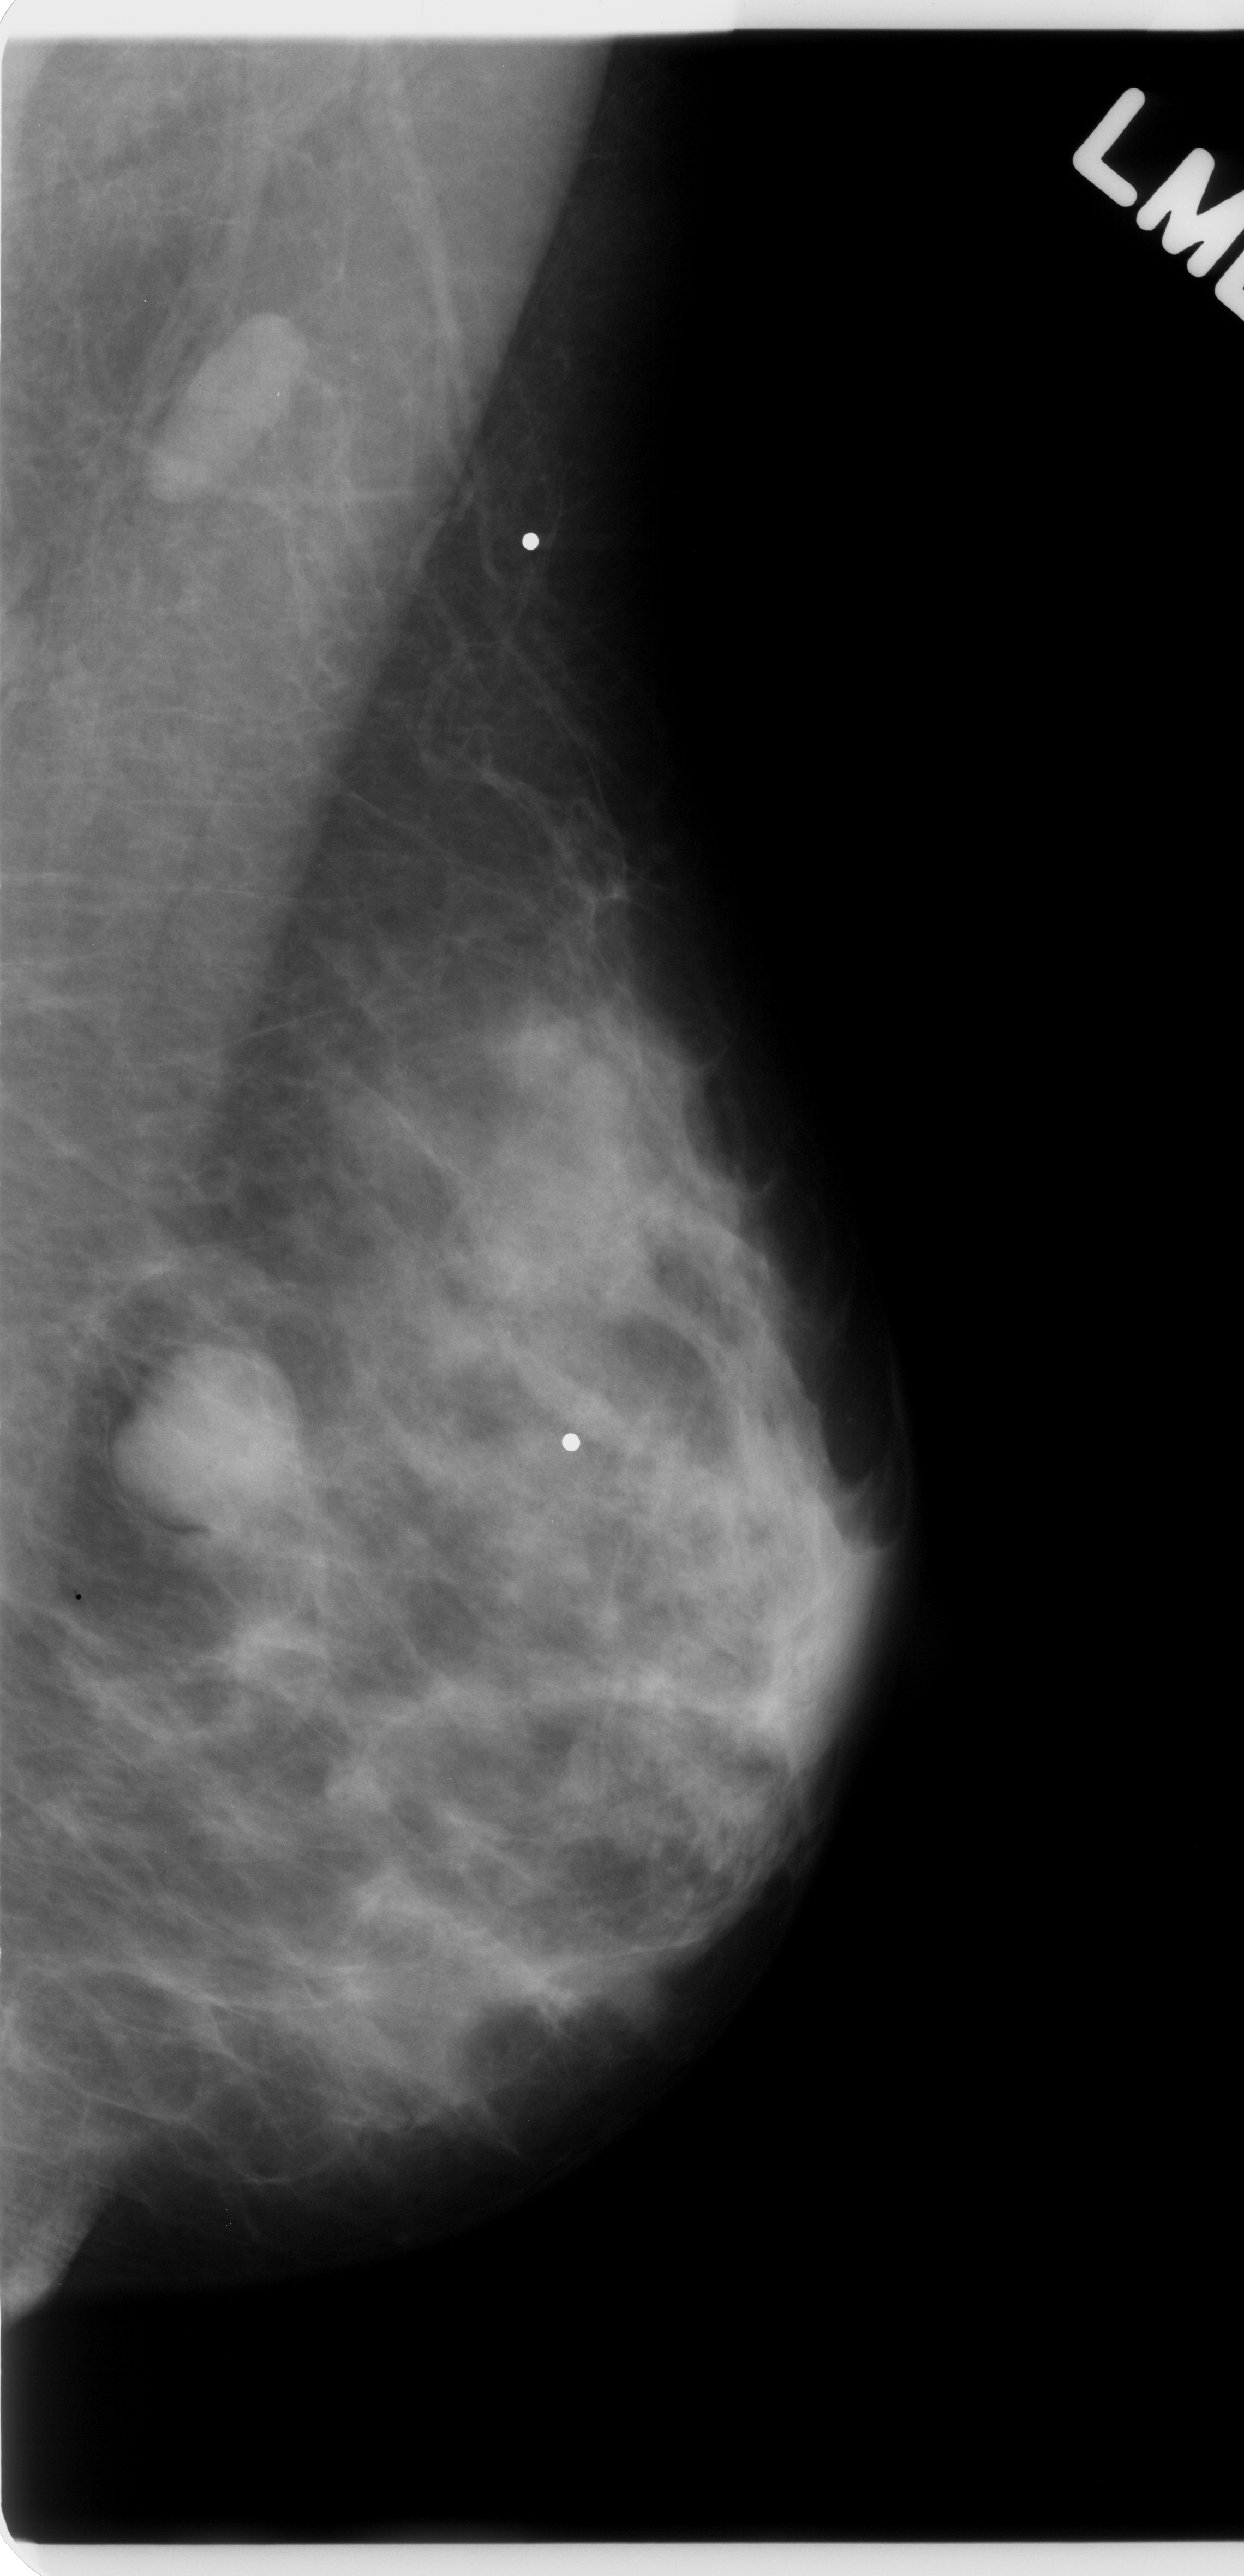
Scanned film-screen mammogram, left breast, MLO view.
Abnormality record for this image: Finding 1 of 2: mass, shape oval, margins circumscribed; BI-RADS assessment category 5; subtlety rating 5 on a 1 (subtle) to 5 (obvious) scale; pathology (as recorded): malignant. Finding 2 of 2: mass, shape round, margins circumscribed; BI-RADS assessment category 4; pathology result (as recorded, not read from the image): malignant.